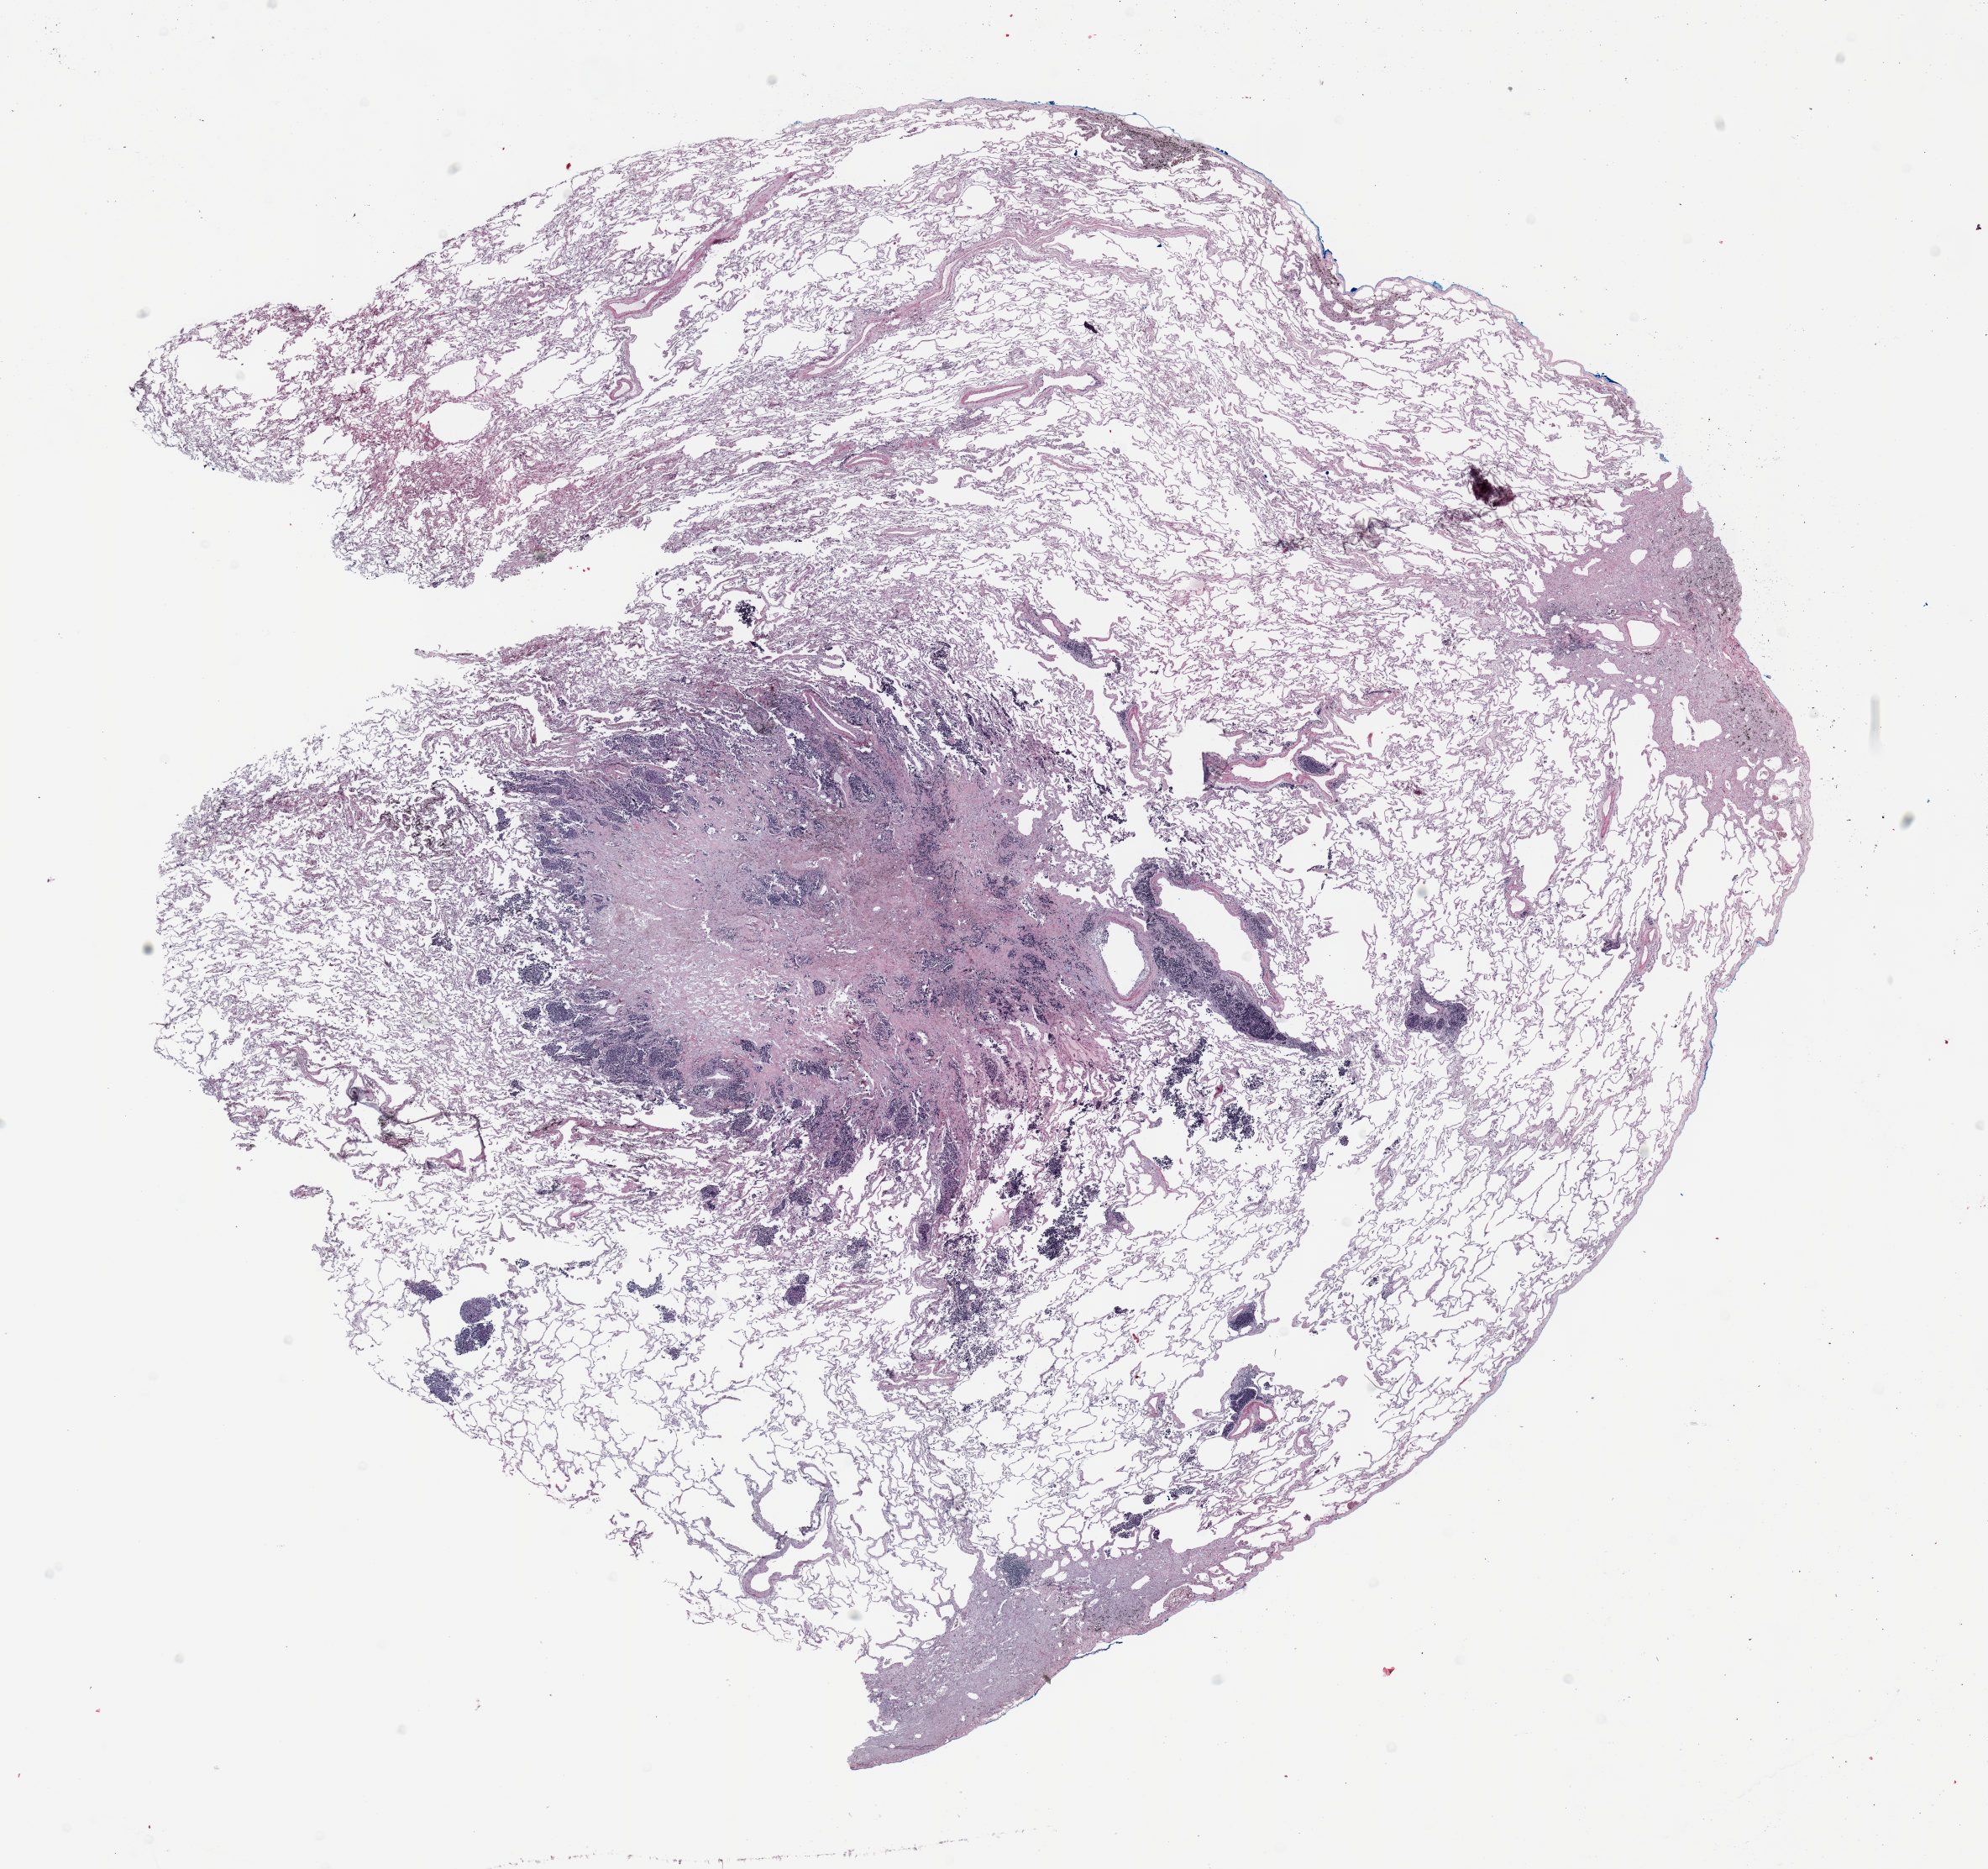
H&E-stained whole-slide image, shown as a low-resolution overview of the whole scanned area (about 19.0 x 17.9 mm), FFPE section, lung. Male, age 67 at enrolment. Former smoker at enrolment. Grade: moderately differentiated (G2).
* tumour size (pathology): 10 mm
* participant's lung-cancer diagnosis: Atypical carcinoid tumor
* primary tumour location (clinical record): left upper lobe
* stage (AJCC 6th edition): IA